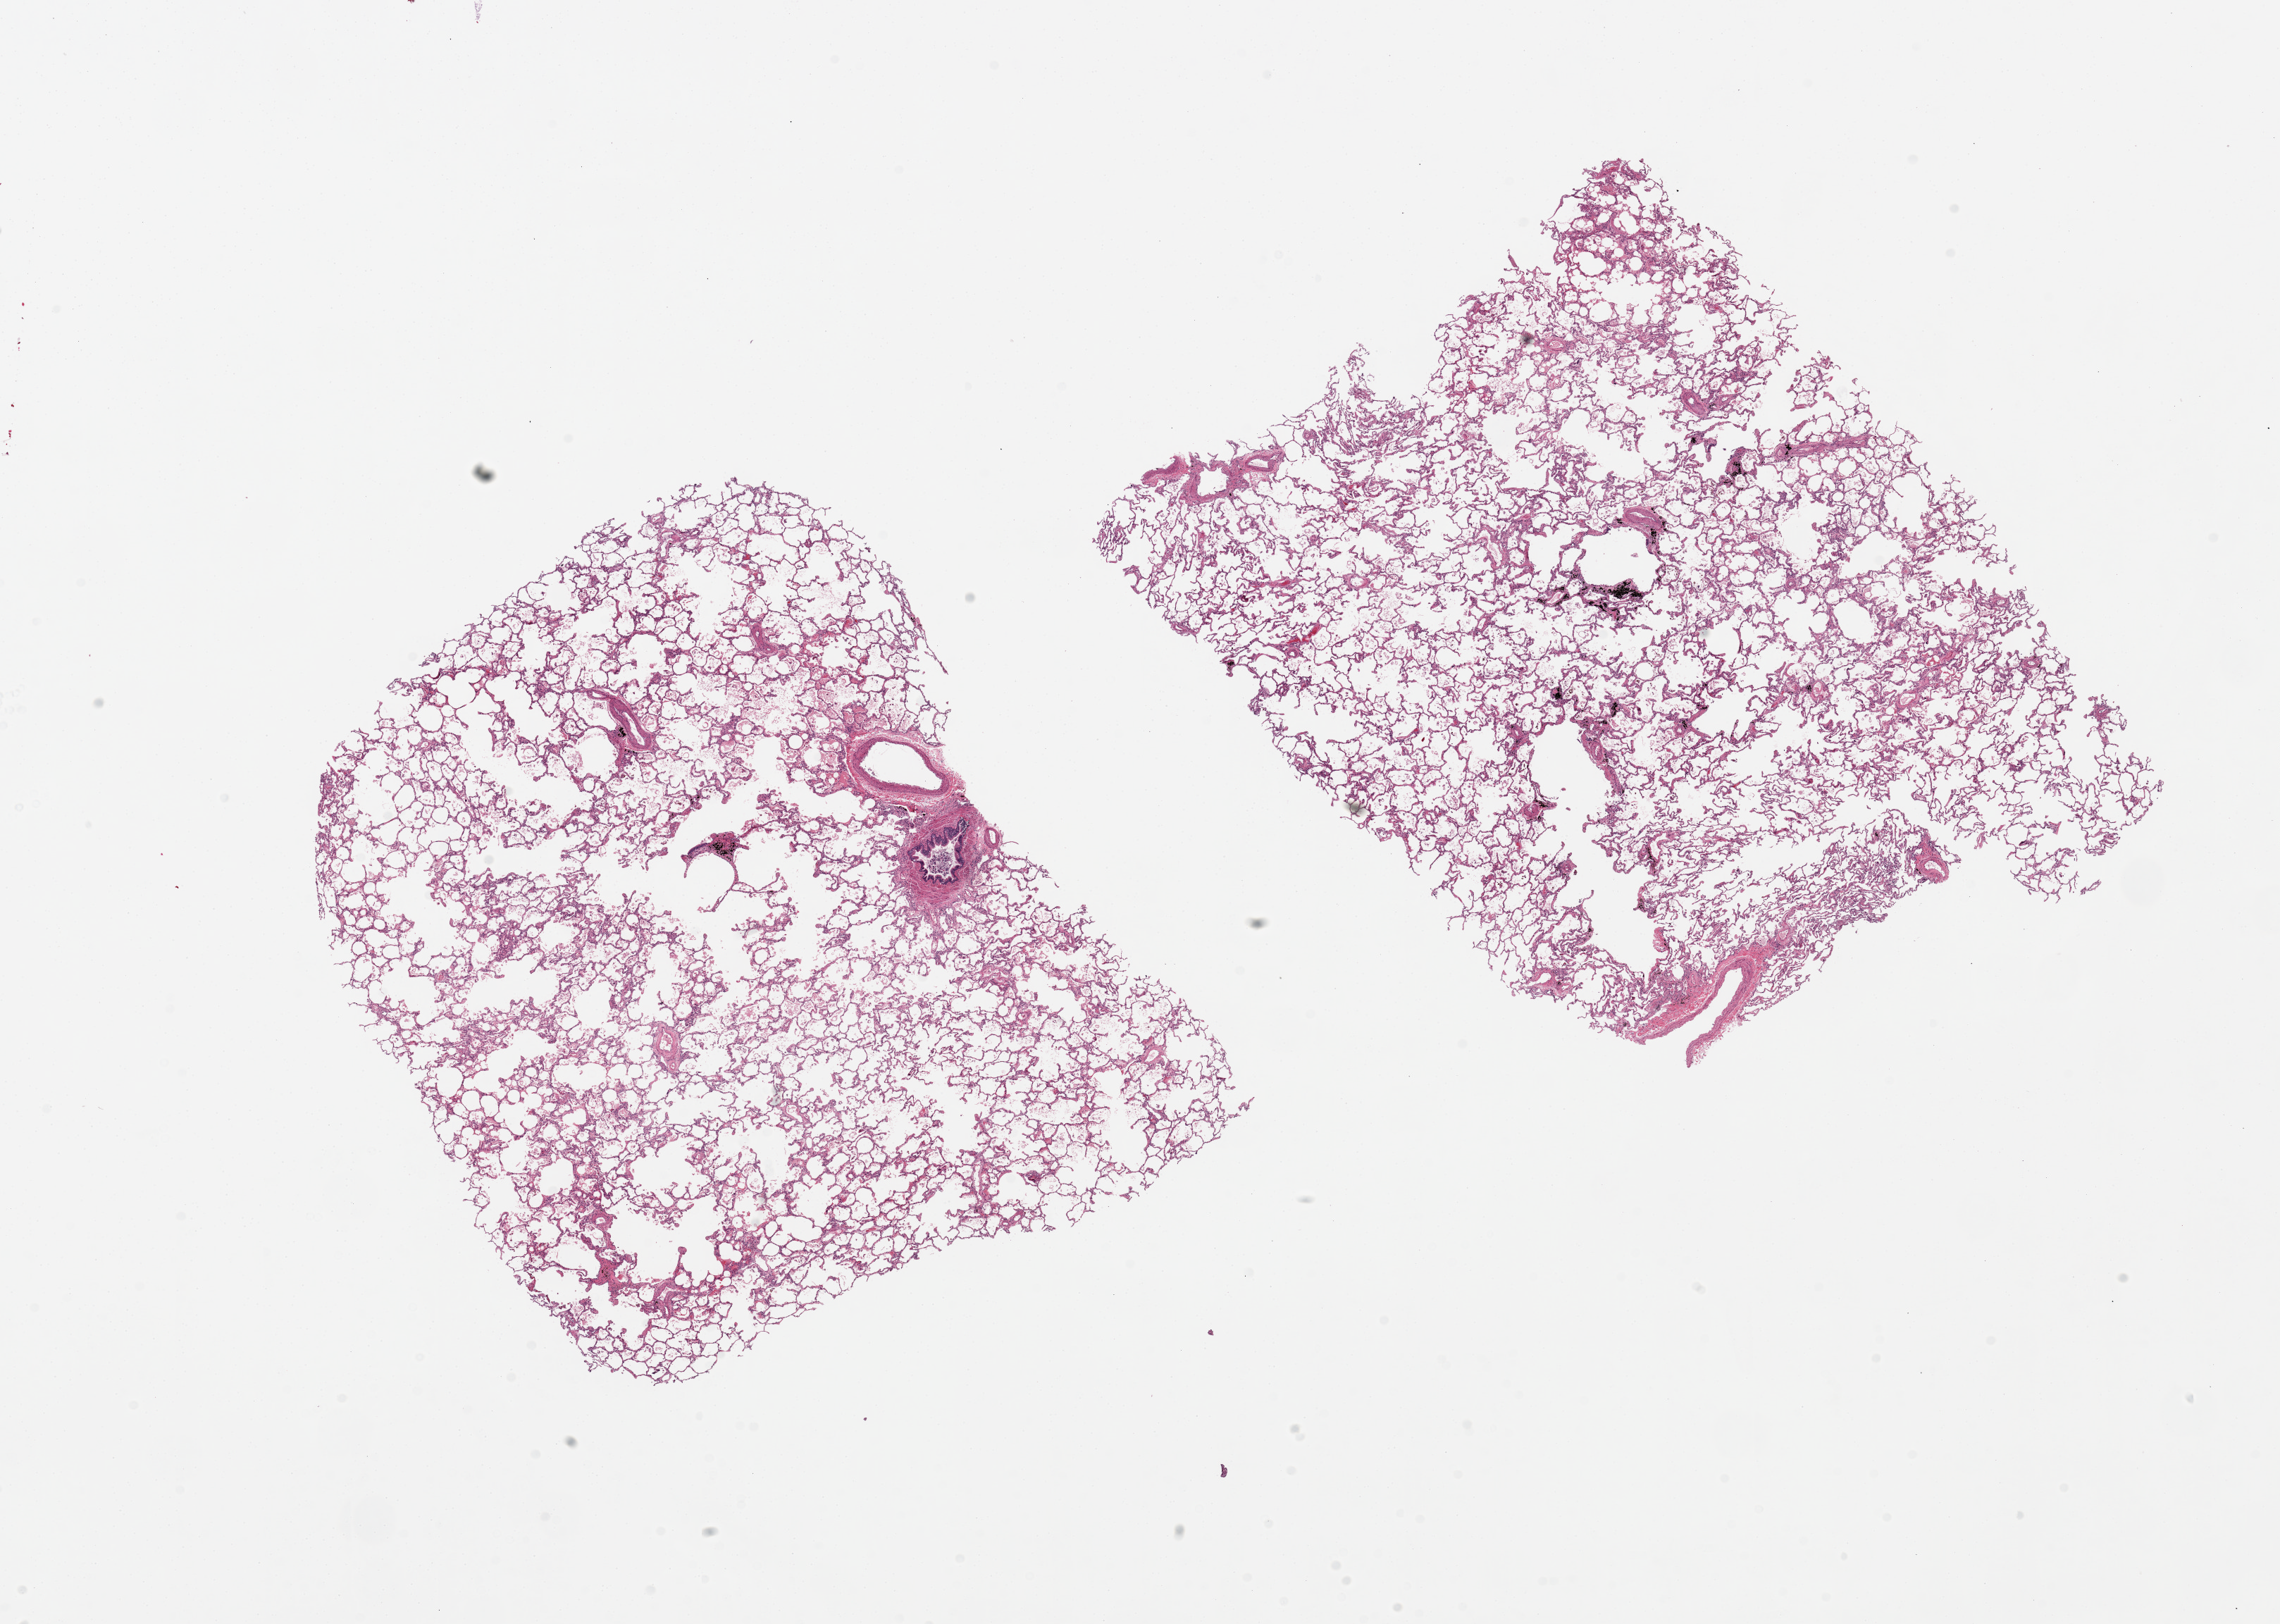
Whole-slide image, haematoxylin and eosin stain, low-resolution overview of the scanned area, about 25.6 x 18.2 mm (slide scanned at 20x); PAXgene-fixed paraffin-embedded (PFPE) section; target tissue: lung; donor tissue sample. Female donor.
Review note (as recorded): 2 pieces, 10x8 & 10x8mm. Panacinar emphysema. Carbon deposits.